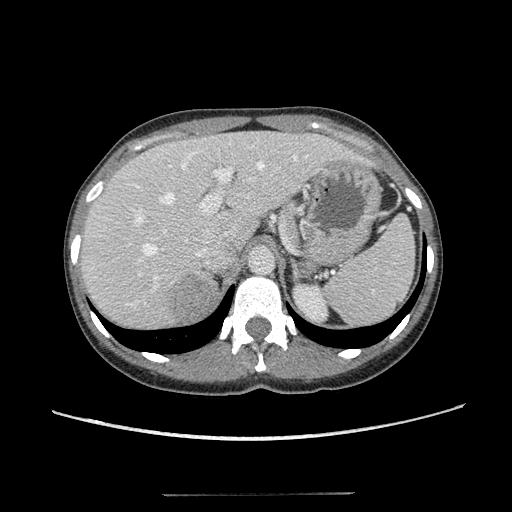
Contrast-enhanced abdominal CT, one axial slice. Position 82 of 117 along the scan axis. Reconstruction kernel STANDARD. 120 kVp. Intravenous contrast given. Soft-tissue window (W 400 / L 40 HU). 512 × 512 image matrix. Female patient, age 35 years. From the clinical record (not read from this slice): diagnosis: adrenocortical carcinoma; tumour side: right adrenal.
Outlined on this slice (semi-automatically segmented with operator editing):
- mass: bounding box [x1, y1, x2, y2] px = [163, 273, 213, 321]